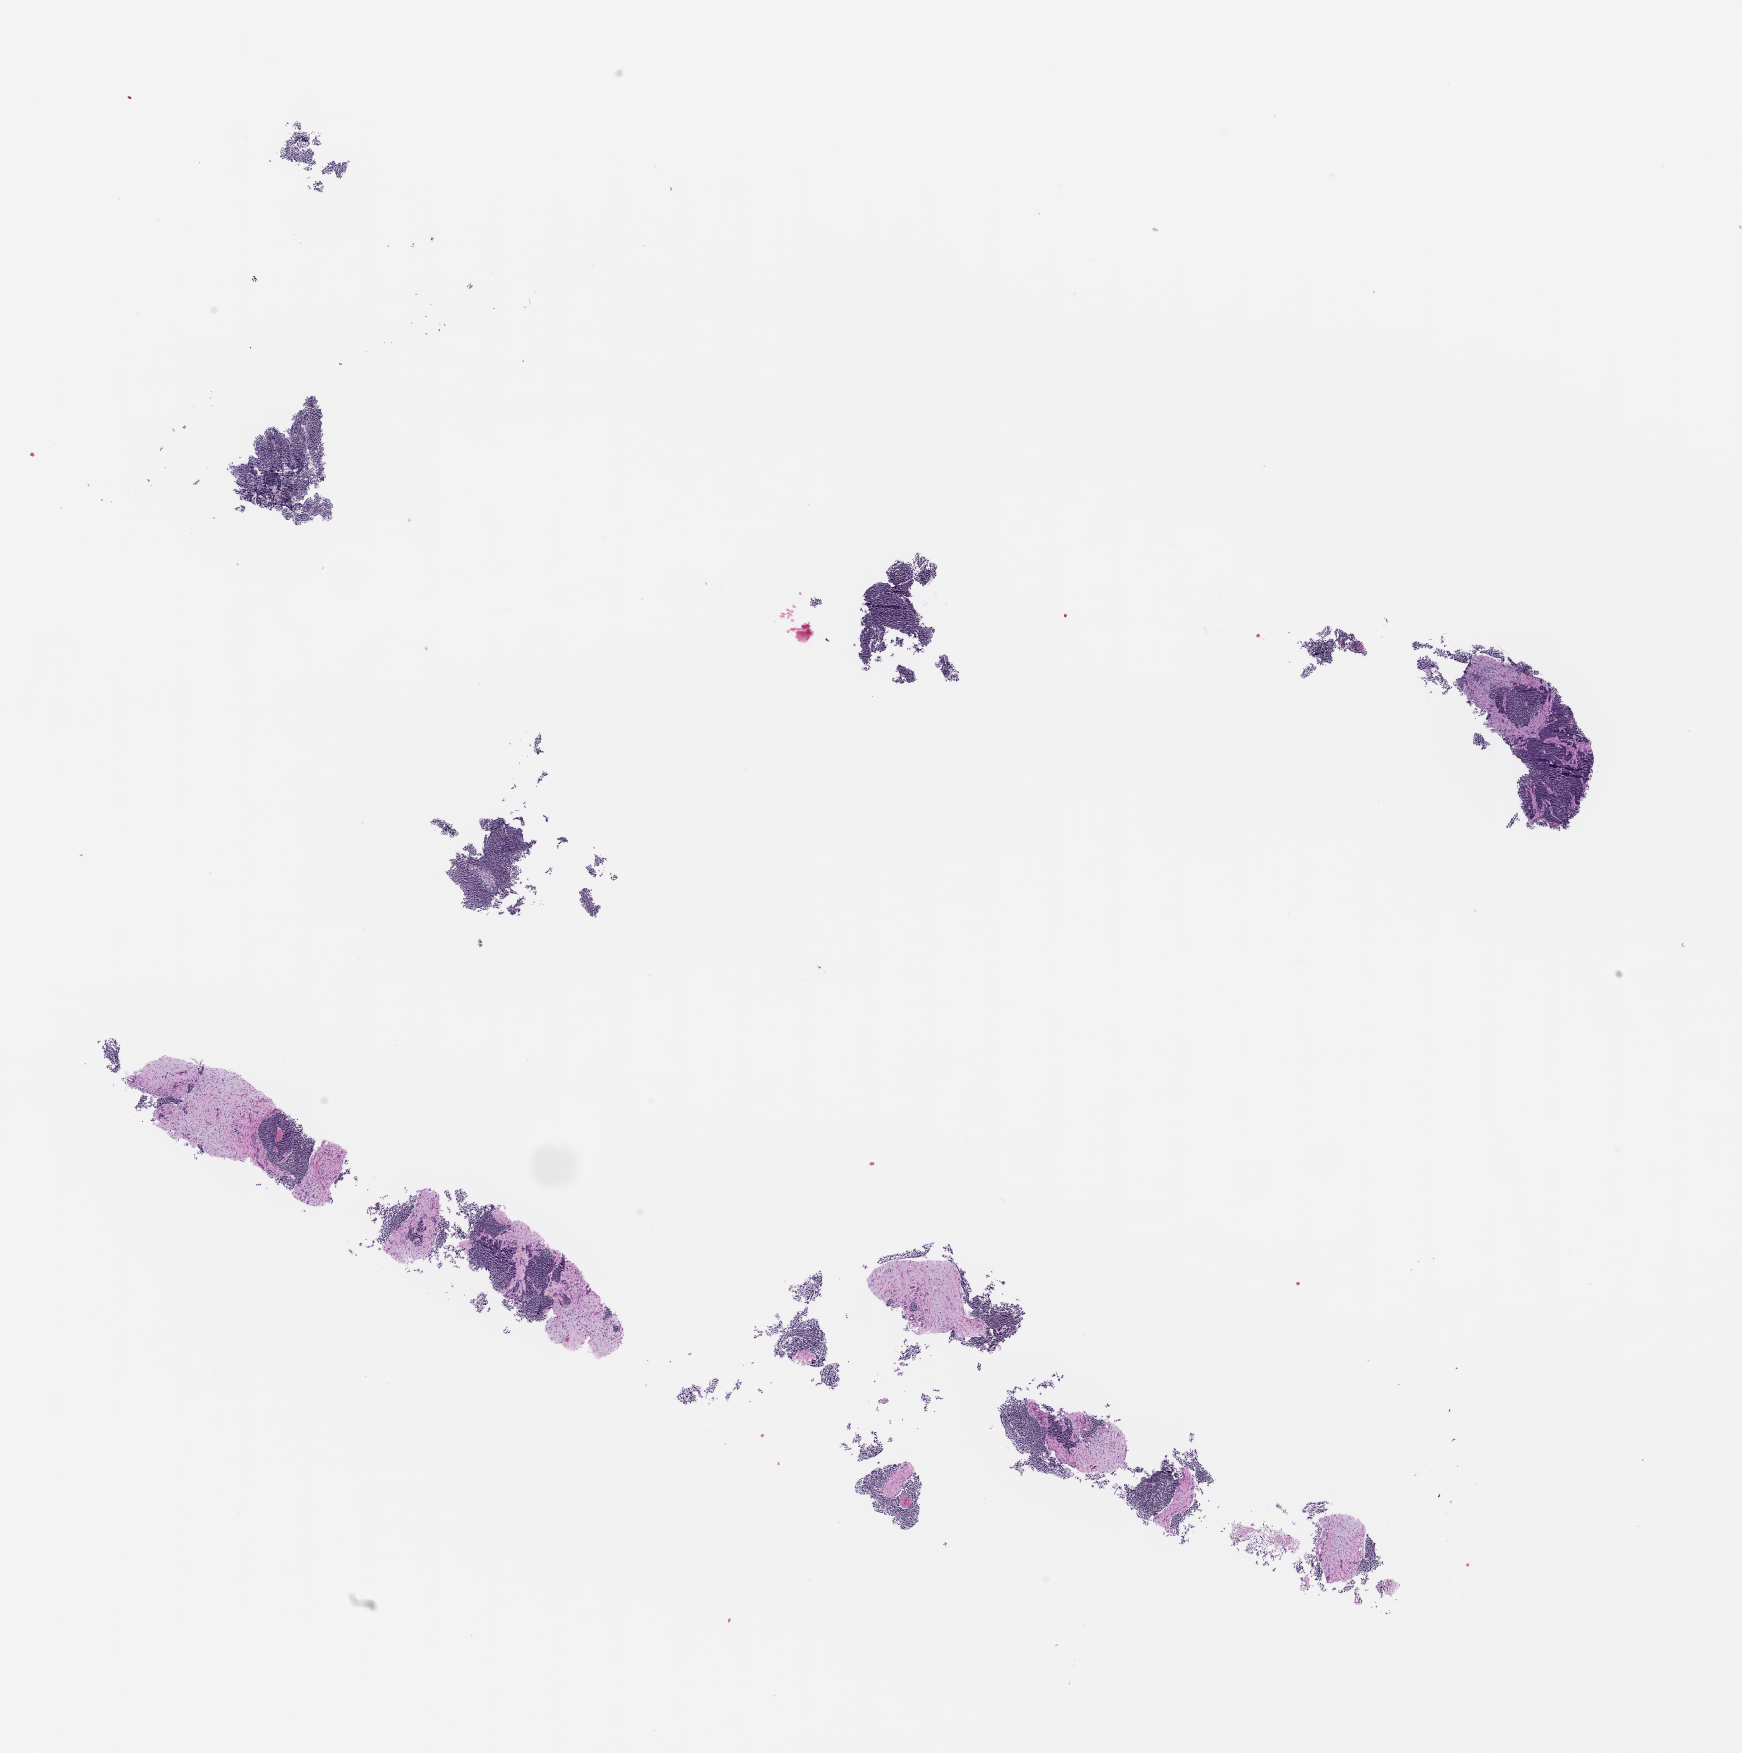
Digitized haematoxylin and eosin-stained section — a low-resolution overview of the entire scanned area, about 14.1 x 14.2 mm. Formalin-fixed, paraffin-embedded (FFPE) tissue. Specimen time point: collected at baseline (before treatment). Male patient.
* this section: metastatic tumor tissue
* patient diagnosis (primary): Small Cell Lung Carcinoma